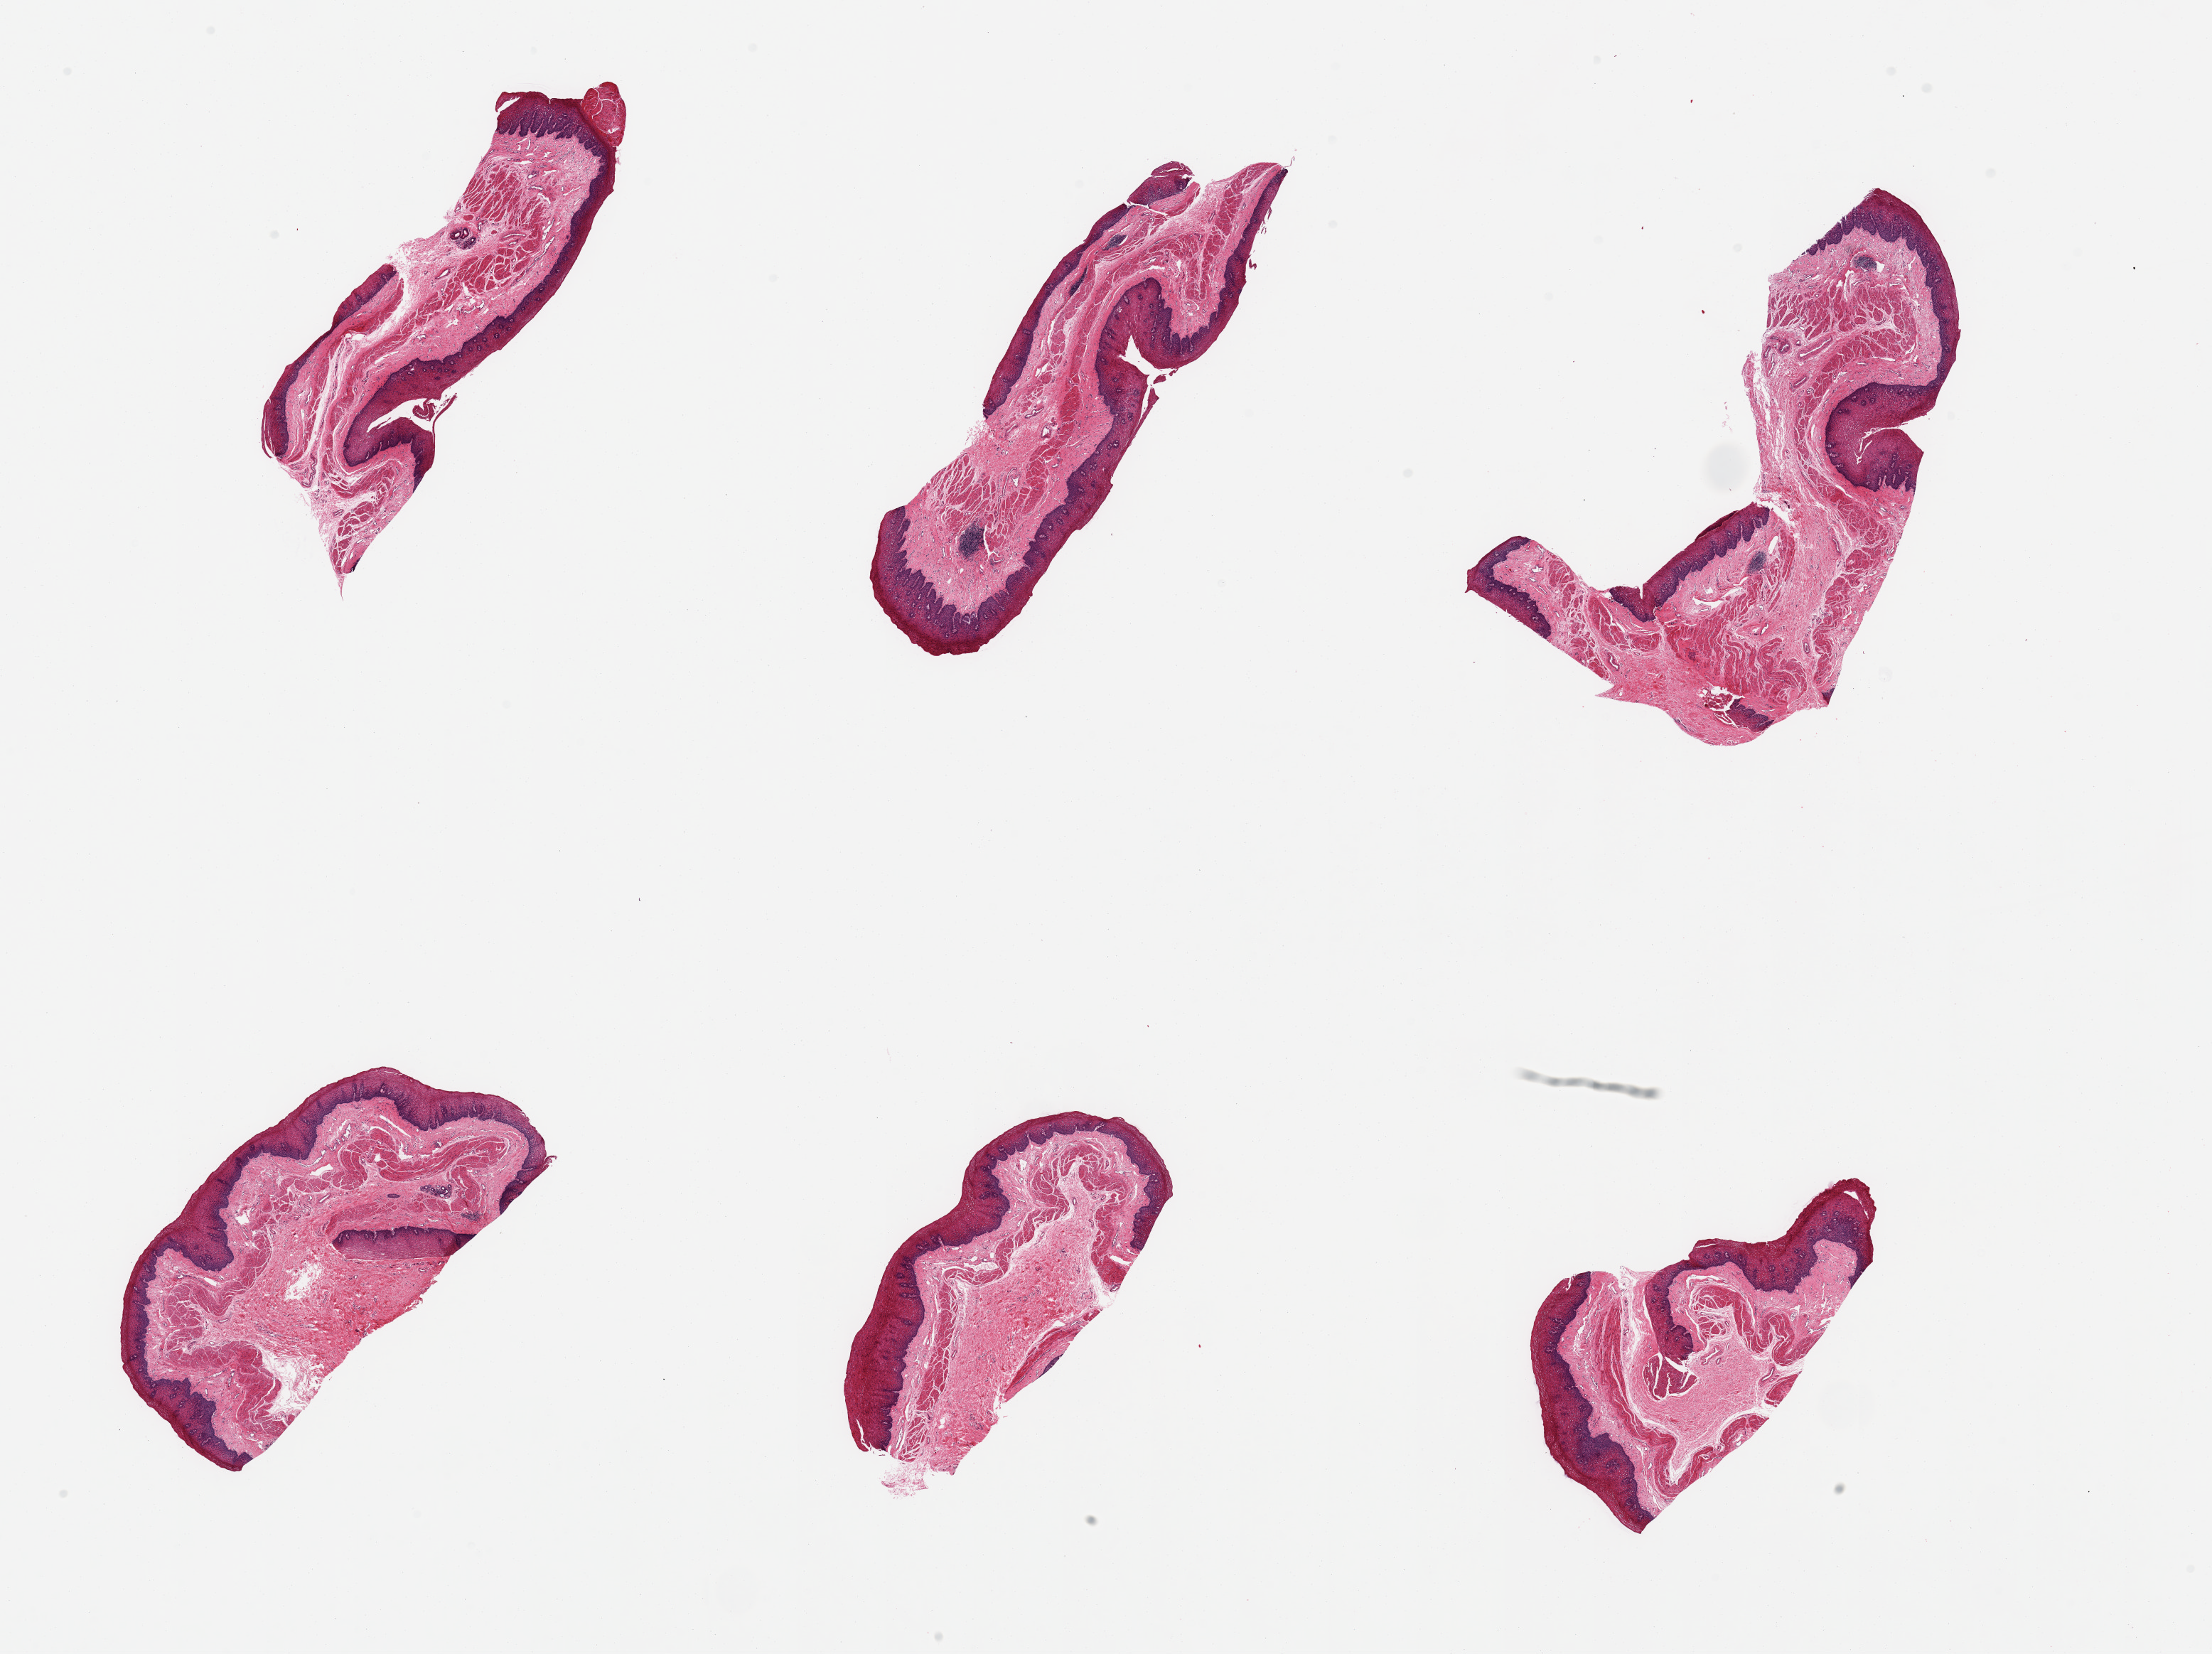
Whole-slide image, haematoxylin and eosin stain, brightfield — a low-resolution overview of the entire scanned area, about 24.6 x 18.4 mm (from a 20x scan); PAXgene-fixed paraffin-embedded (PFPE) section; section of esophageal mucous membrane (target tissue); donor tissue sample. Donor sex: female.
Reviewer comment on this tissue sample: 6 pieces.